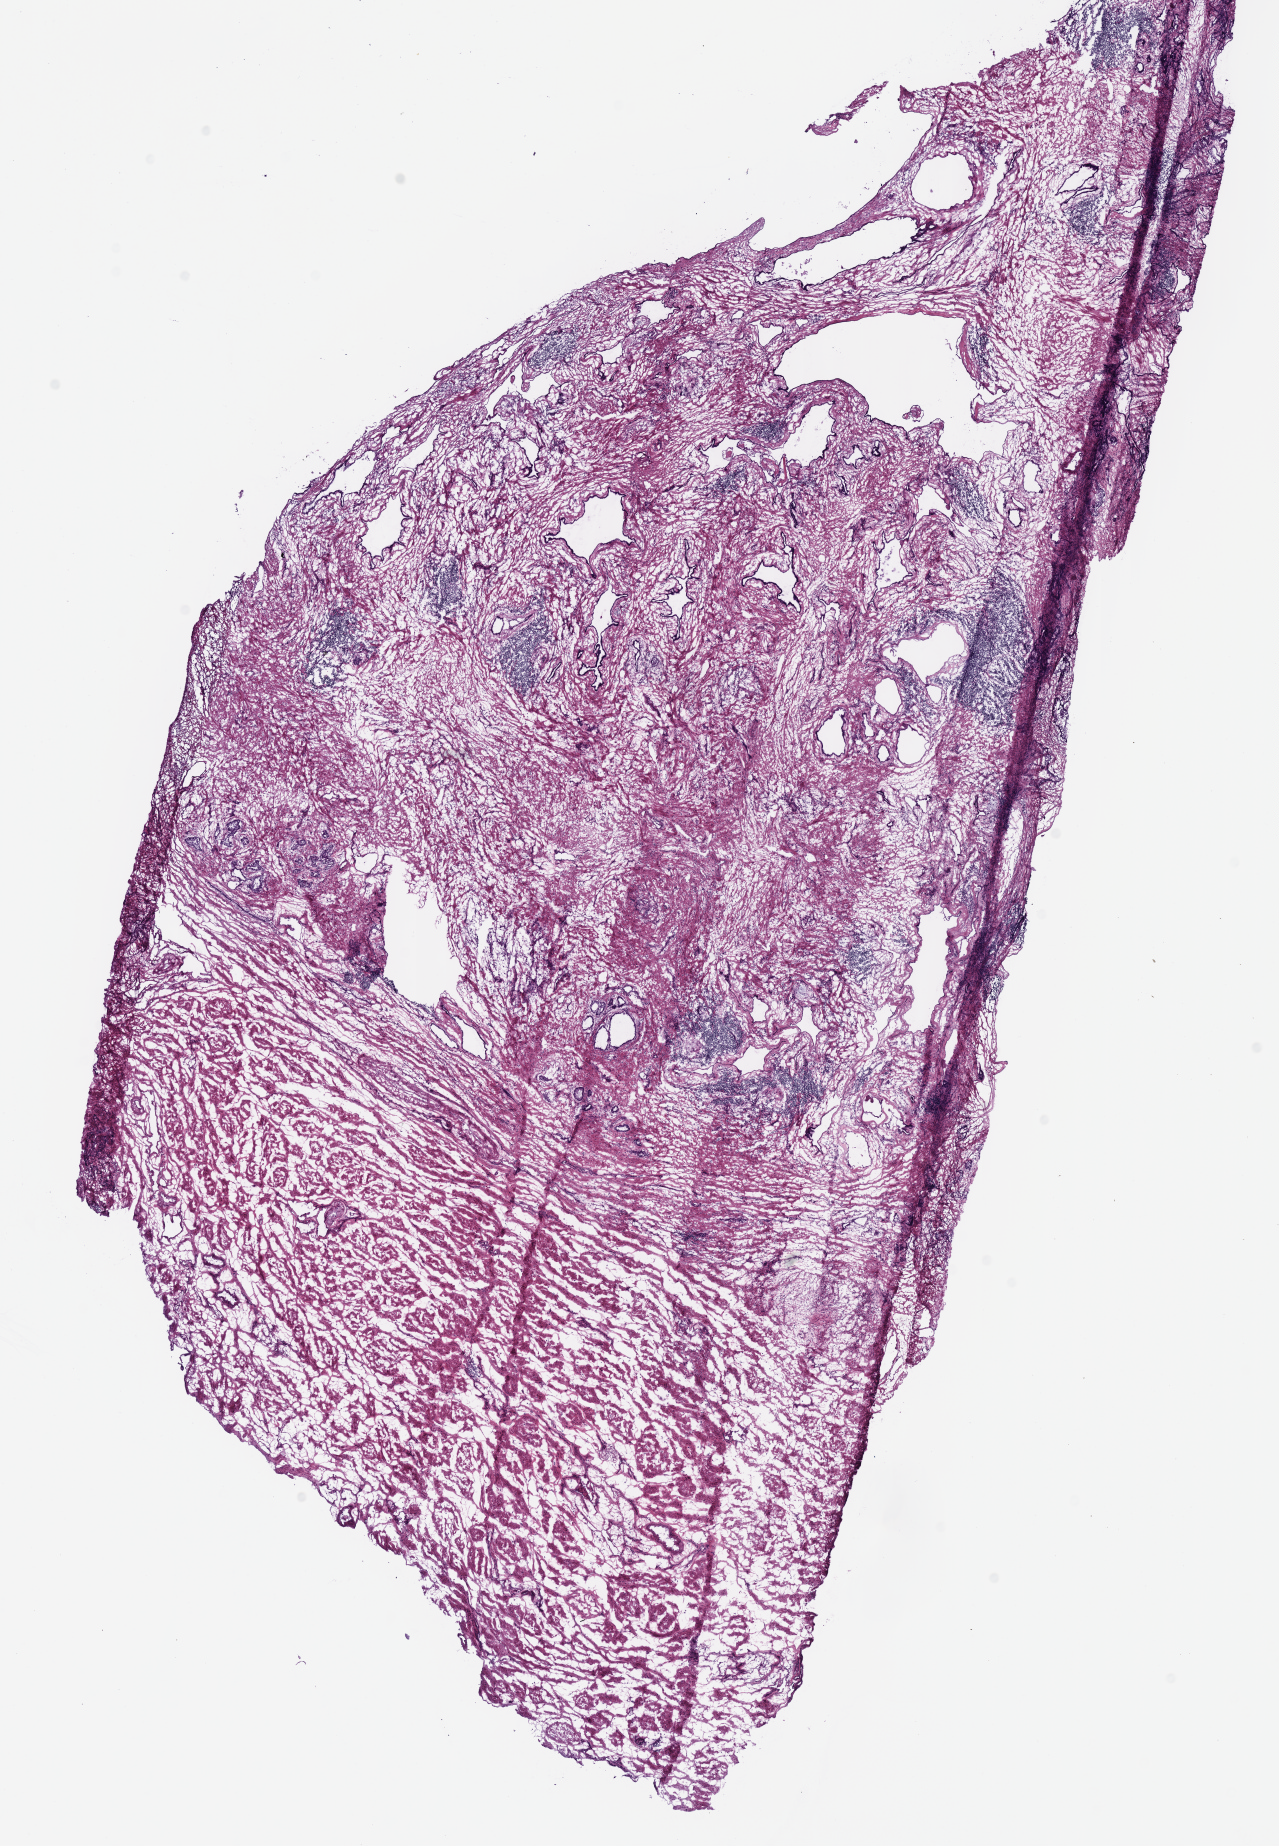
Digitized H&E-stained tissue section (whole slide) — shown as a low-resolution overview of the whole scanned area (about 10.1 x 14.5 mm). Frozen section. Sample: solid tissue normal (non-tumour tissue), prostate. Male patient; age at initial diagnosis 68 years.
This section: solid tissue normal sample (biorepository sample class). Patient diagnosis: Acinar cell carcinoma (prostate gland).